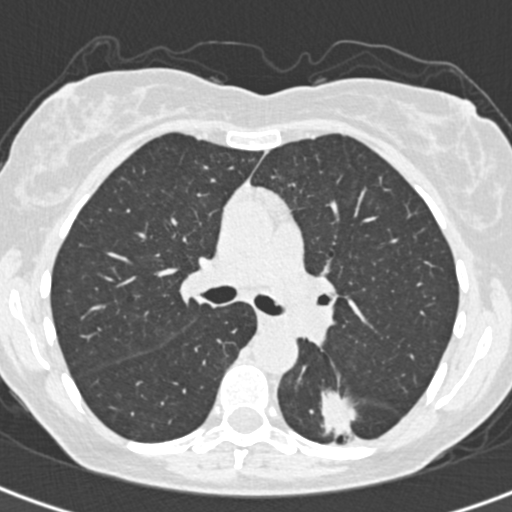
Low-dose screening chest CT, one axial slice; position 207 of 328 along the scan axis; lung window (W 1500 / L -600 HU); 512 × 512 image matrix, field of view 284 × 284 mm.
Outlined on this slice (manually delineated by an expert):
- lesion 1 (tumor, lower lobe of left lung): box from (x=321, y=390) to (x=357, y=438) px